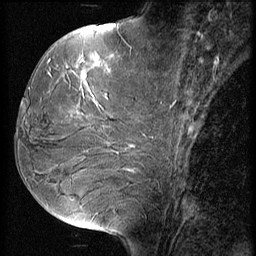
Breast MRI (dynamic contrast-enhanced), one sagittal slice; slice 25 of 56 in the series (ordered by position); 3 images stored at this slice position (order not interpretable as contrast timing); 1.5 T; TE 4.2 ms, TR 9 ms; 2.5 mm slice thickness; 256 × 256 image matrix, field of view 180 × 180 mm. Female patient, age 51 years. From the clinical record (not read from this slice): setting: breast cancer imaged before/during neoadjuvant chemotherapy; receptor status: HR-positive, HER2-negative.
Outlined on this slice (semi-automatic segmentation, software-assisted and operator-edited):
- analysis volume of interest (the breast-tissue region the enhancement analysis was run in; not a lesion): bounding box [x1, y1, x2, y2] px = [23, 56, 156, 165]
- tumour enhancement mask (voxels above the 140 % enhancement threshold inside the analysis volume of interest): [77, 56, 109, 117]